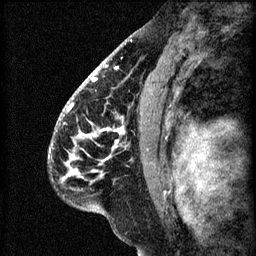
Breast MRI (dynamic contrast-enhanced), one sagittal slice. Position 39 of 60 along the scan axis. 3 images stored at this slice position (order not interpretable as contrast timing). 1.5 T. TE 4.2 ms, TR 8.2 ms. 256 × 256 image matrix, field of view 180 × 180 mm. Female patient, age 41 years.
Outlined on this slice (semi-automatically segmented with operator editing):
- analysis volume of interest (the breast-tissue region the enhancement analysis was run in; not a lesion): box from (x=56, y=104) to (x=157, y=207) px
- tumour enhancement mask (voxels above the 70 % enhancement threshold inside the analysis volume of interest): (x=68, y=106)–(x=124, y=177)